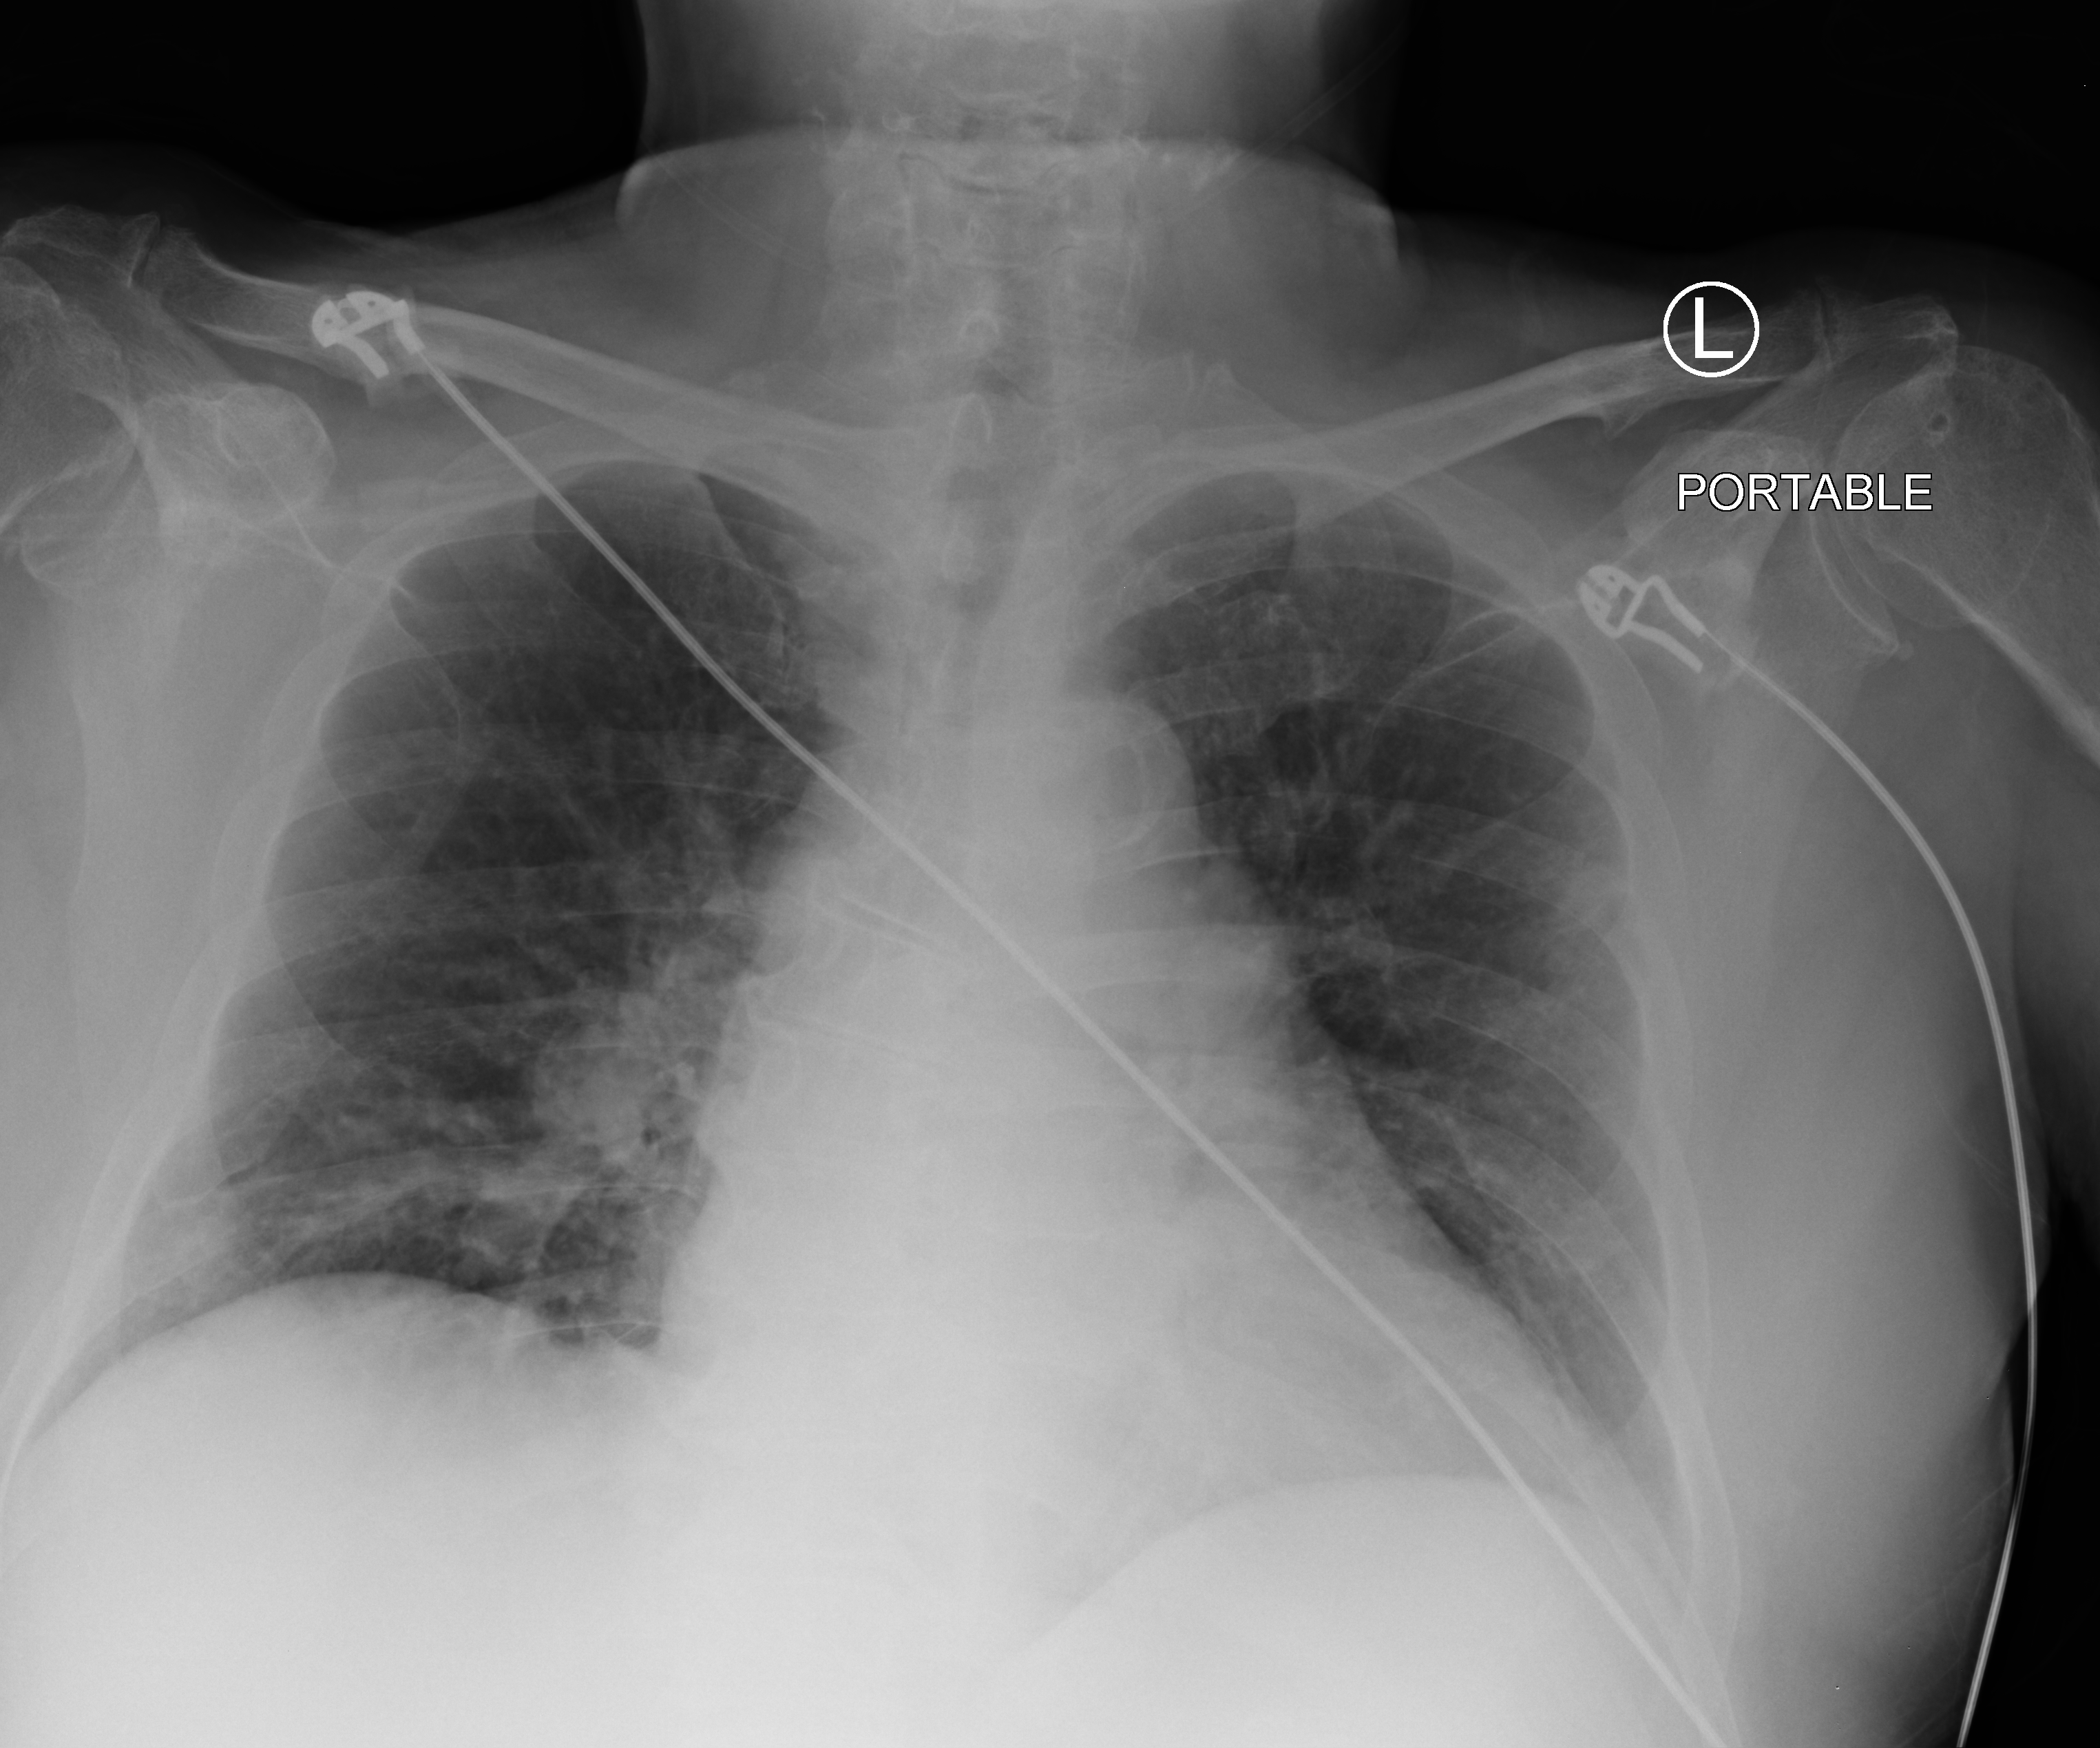
Chest X-ray (portable), anteroposterior (AP) projection. Male patient hospitalised with COVID-19, age 60–74 years.
Hospital-stay facts (about this admission, not read from this image; timing relative to this image not recorded): diabetes (admission record): no; mechanically ventilated during this hospital stay: no.